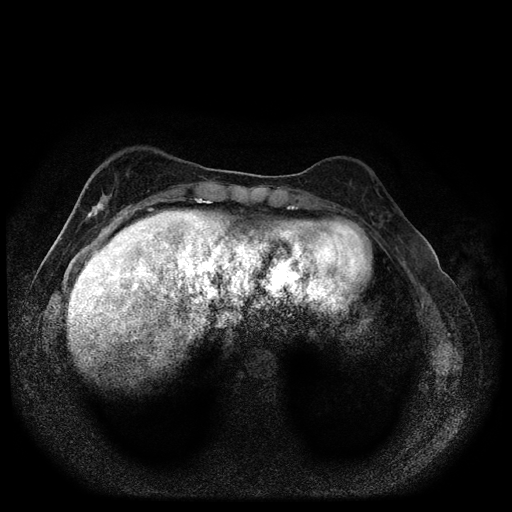
Breast MRI (dynamic contrast-enhanced, multi-phase), one axial slice. Slice 27 of 116 in the series (ordered by position). Dynamic contrast-enhanced series, time point 2 of 5 at this slice position (early post-contrast). 1.5 T. TE 2.7 ms, TR 5.4 ms. 2 mm slice thickness. 512 × 512 image matrix, field of view 330 × 330 mm. Female patient, age 49 years.
Annotated regions visible in this slice (semi-automatic segmentation, software-assisted and operator-edited):
- breast lesion (labelled 'tumour' in the annotation; benign lesions carry a separate 'benign' label): bounding box (x1, y1, x2, y2) in pixels: (82, 191, 114, 224)